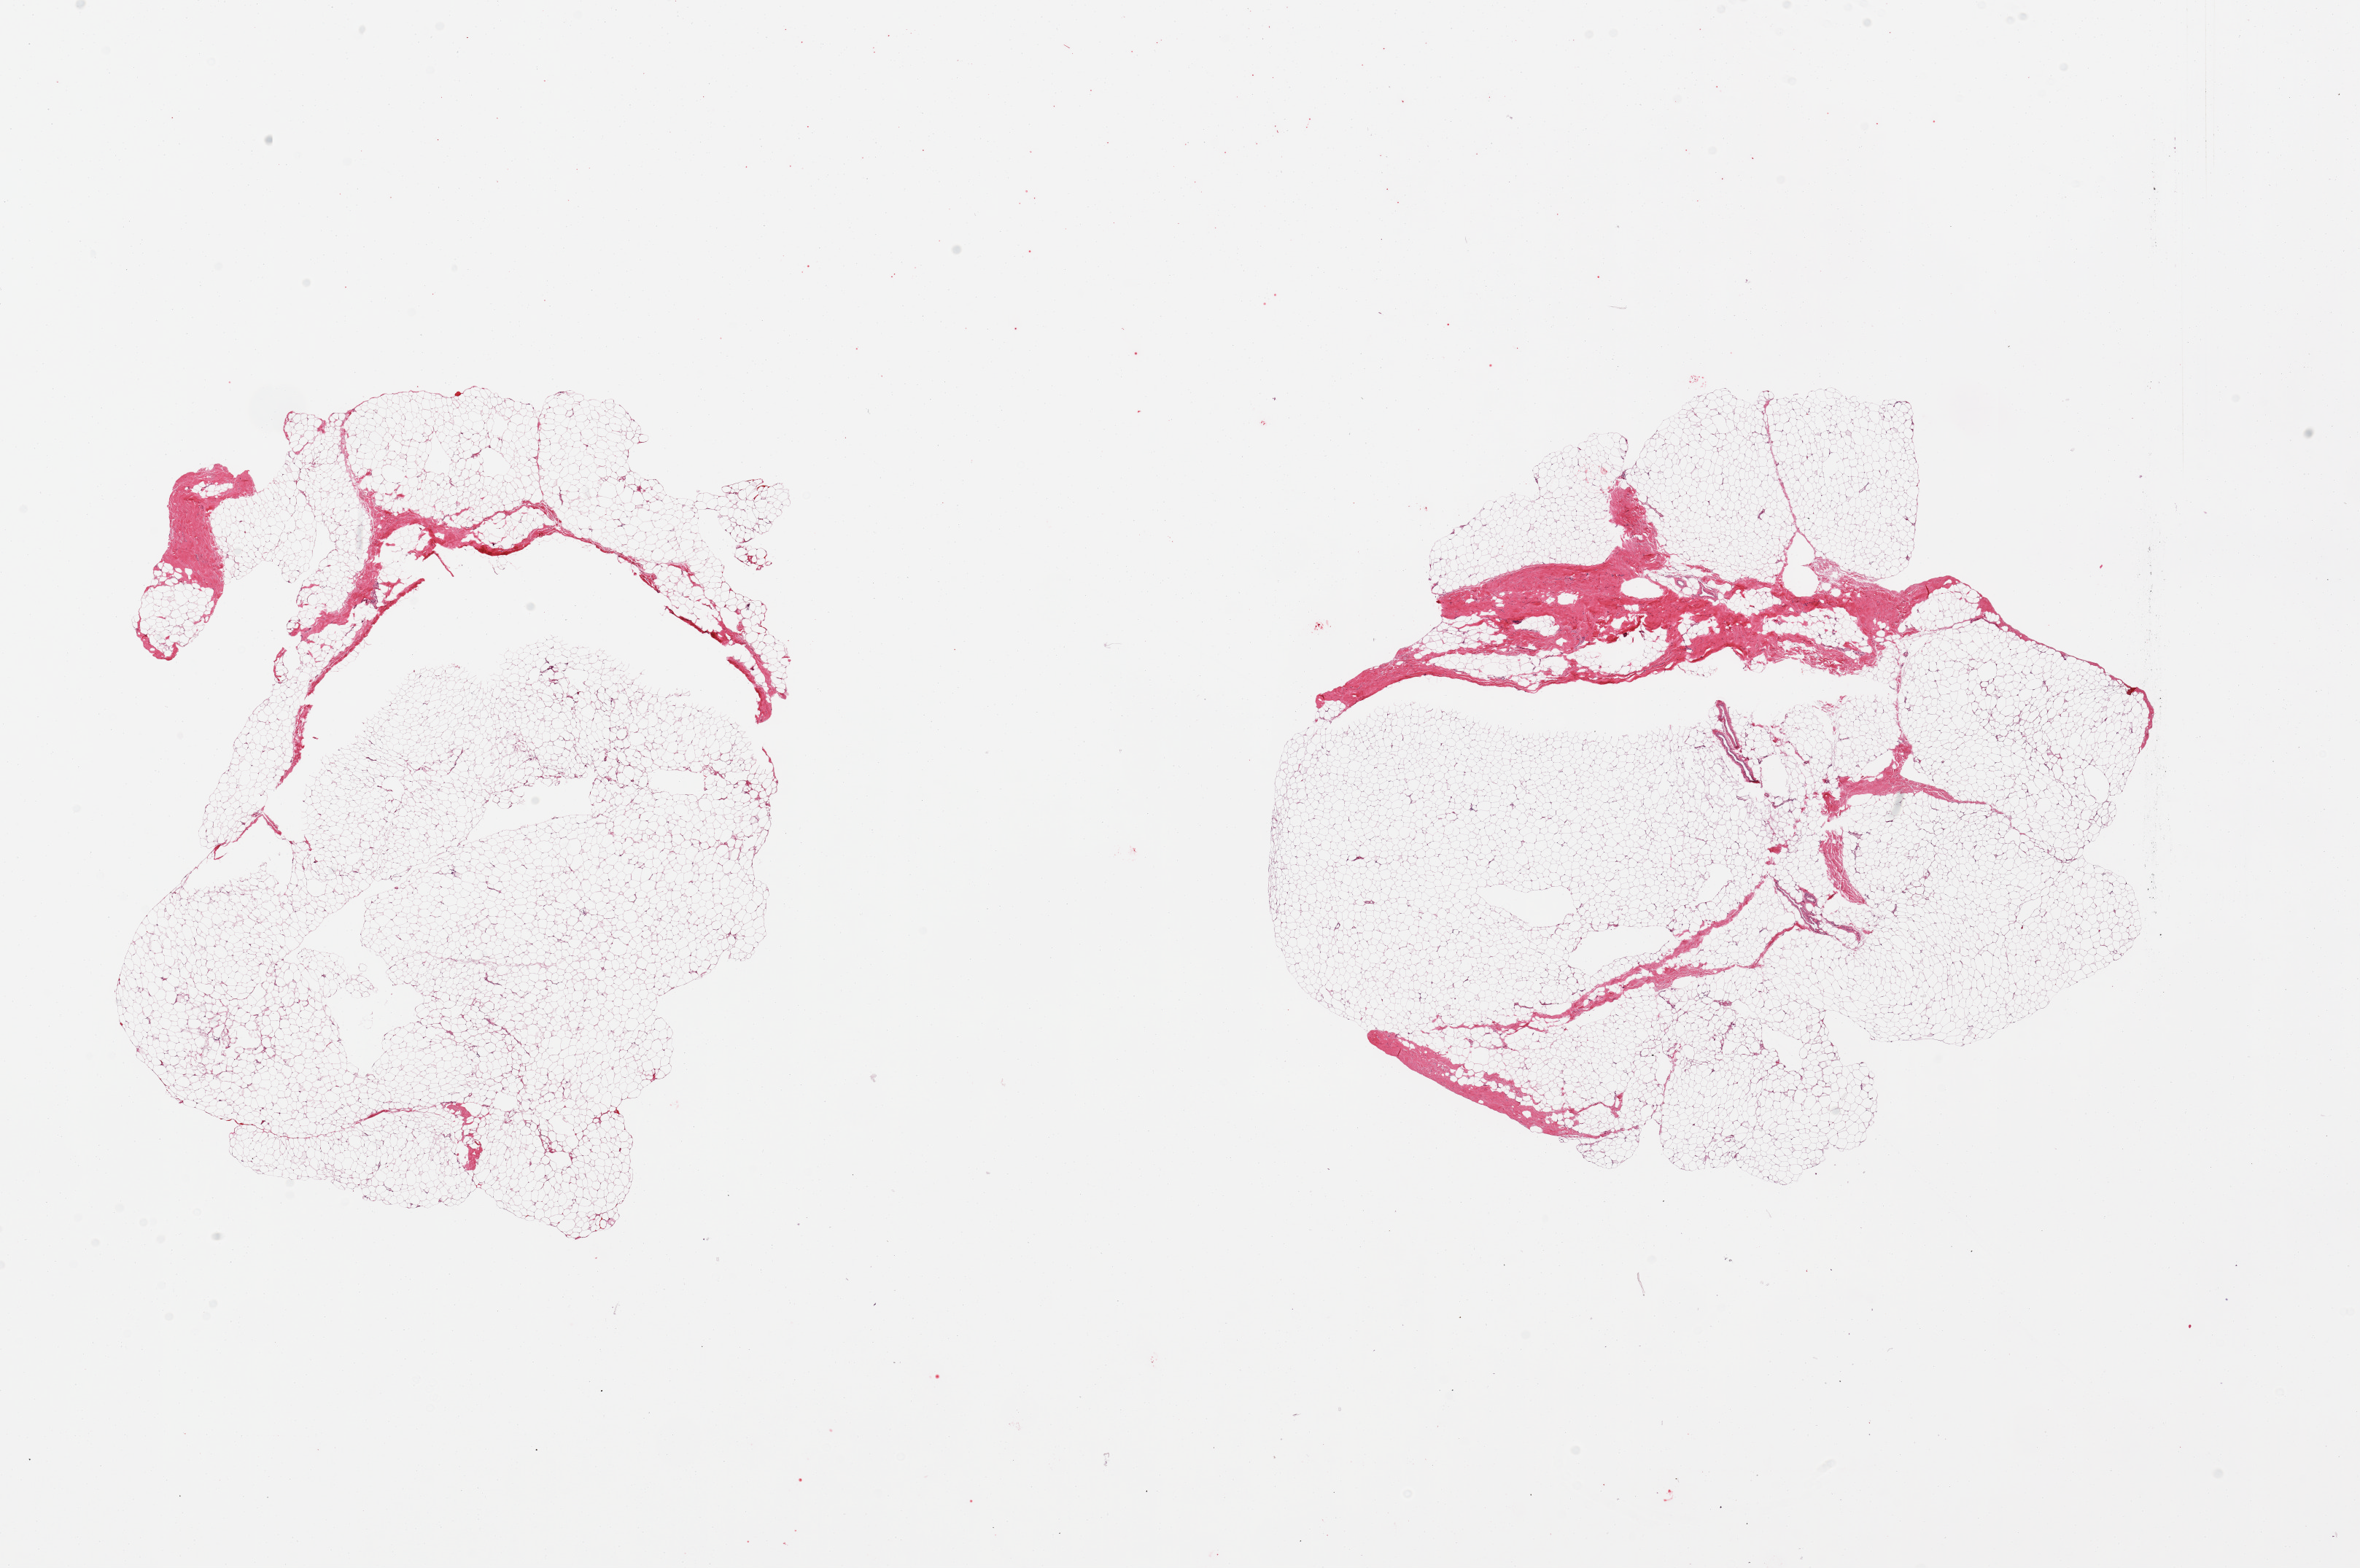
Whole-slide image, H&E stain, brightfield — low-resolution overview of the scanned area, about 25.6 x 17.0 mm; PAXgene-fixed paraffin-embedded (PFPE) section; section of breast (target tissue); donor tissue sample.
• review note (as recorded): 2 pieces; mature adipose tissue and 5 to 10% fibrovascular component; no ductal structures